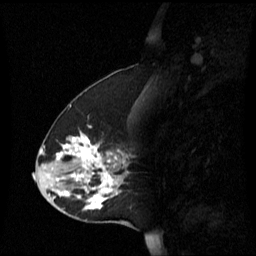
Breast MRI (dynamic contrast-enhanced), one sagittal slice; slice 25 of 60 in the series (ordered by position); dynamic contrast-enhanced series, image 2 of 3 at this slice position (ordered by acquisition); 1.5 T; TE 4.2 ms, TR 8.4 ms; 2.2 mm slice thickness; 256 × 256 image matrix, field of view 240 × 240 mm. Female patient, age 45 years. From the clinical record (not read from this slice): setting: breast cancer imaged before/during neoadjuvant chemotherapy; receptor status: HR-positive, HER2-negative.
Outlined on this slice (semi-automatic segmentation, software-assisted and operator-edited):
- analysis volume of interest (the breast-tissue region the enhancement analysis was run in; not a lesion): box from (x=38, y=126) to (x=131, y=221) px
- tumour enhancement mask (voxels above the 70 % enhancement threshold inside the analysis volume of interest): (x=48, y=126)–(x=119, y=209)